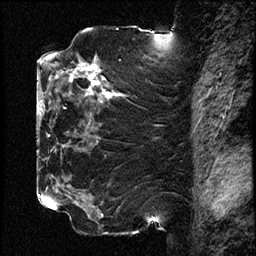
Breast MRI (dynamic contrast-enhanced), one sagittal slice. Slice 45 of 78 in the series (ordered by position). Dynamic contrast-enhanced study with each time point stored as its own series, time point 2 of 3 at this slice position (early post-contrast, ordered by acquisition time). 1.5 T. TE 4.2 ms, TR 17.6 ms. 2 mm slice thickness. 256 × 256 image matrix. Female patient, age 42 years. From the clinical record (not read from this slice): setting: breast cancer imaged before/during neoadjuvant chemotherapy; receptor status: HER2-positive.
Outlined on this slice (semi-automatic segmentation, software-assisted and operator-edited):
- analysis volume of interest (the breast-tissue region the enhancement analysis was run in; not a lesion): bounding box [x1, y1, x2, y2] px = [50, 48, 113, 129]
- tumour enhancement mask (voxels above the 100 % enhancement threshold inside the analysis volume of interest): [71, 63, 109, 97]